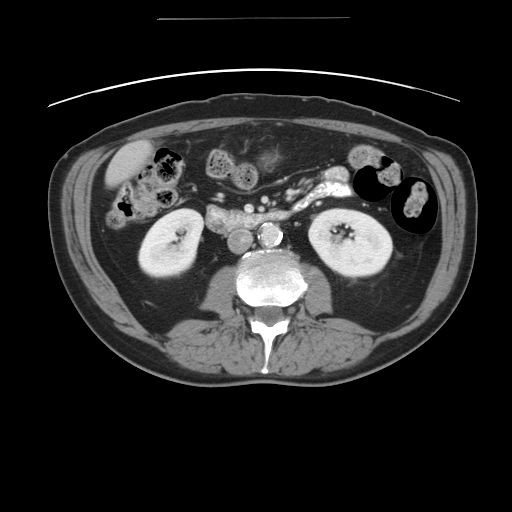
Contrast-enhanced abdominal CT, one axial slice. Slice 12 of 49 in the series (ordered by position). Reconstruction kernel STANDARD. 120 kVp. Intravenous contrast given. Soft-tissue window (W 400 / L 40 HU). 512 × 512 image matrix. Male patient, age 57 years. Case-level facts recorded for this patient, not image findings: diagnosis: colorectal cancer liver metastases, imaged before liver resection; multiple liver metastases: yes; largest metastasis: 4 cm.
Structures marked on this image (manually delineated by an expert):
- liver: box from (x=105, y=140) to (x=152, y=185) px